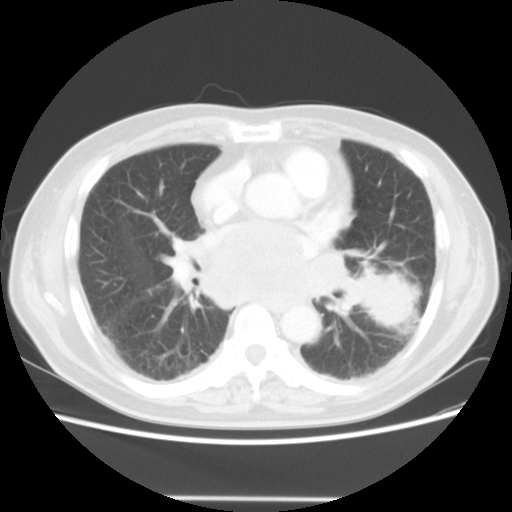
Chest CT, one axial slice; slice 24 of 56 in the series (ordered by position); reconstruction kernel STANDARD; lung window (W 1500 / L -600 HU); 5 mm slice thickness; 512 × 512 image matrix, field of view 360 × 360 mm. Male patient, age 66 years. Case-level facts recorded for this patient, not image findings: clinical TNM (as recorded): T4 N3 M0.
Outlined on this slice (bounding box drawn by a radiologist):
- lung tumour (recorded histology: small cell carcinoma): bounding box (x1, y1, x2, y2) in pixels: (357, 259, 417, 331)